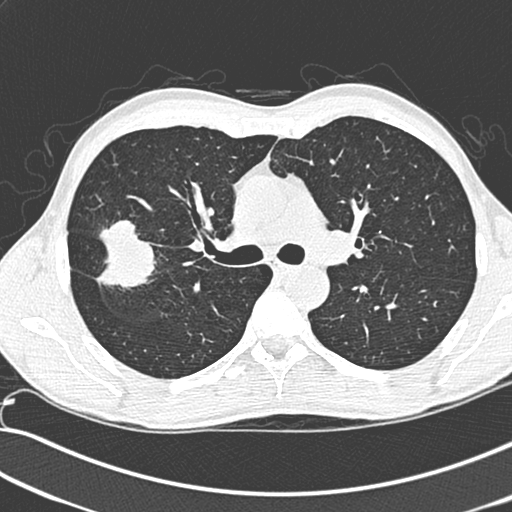
Low-dose screening chest CT, one axial slice; slice 192 of 281 in the series (ordered by position); lung window (W 1500 / L -600 HU); 1.3 mm slice thickness; 512 × 512 image matrix.
Structures marked on this image (manually delineated by an expert):
- lesion 1 (tumor, upper lobe of right lung): bounding box (x1, y1, x2, y2) in pixels: (96, 220, 155, 289)